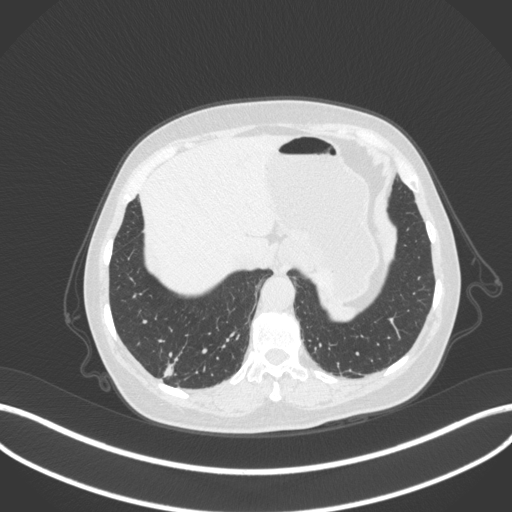
Chest CT, one axial slice. Slice 45 of 340 in the series (ordered by position). Reconstruction kernel B31f. Lung window (W 1500 / L -600 HU). 1 mm slice thickness. 512 × 512 image matrix, field of view 400 × 400 mm. Female patient, age 69 years. Case-level facts recorded for this patient, not image findings: clinical TNM (as recorded): T1b N0 M0.
Annotated regions visible in this slice (rectangle marked by the reading radiologist):
- lung tumour (recorded histology: adenocarcinoma): bounding box (x1, y1, x2, y2) in pixels: (162, 361, 174, 377)